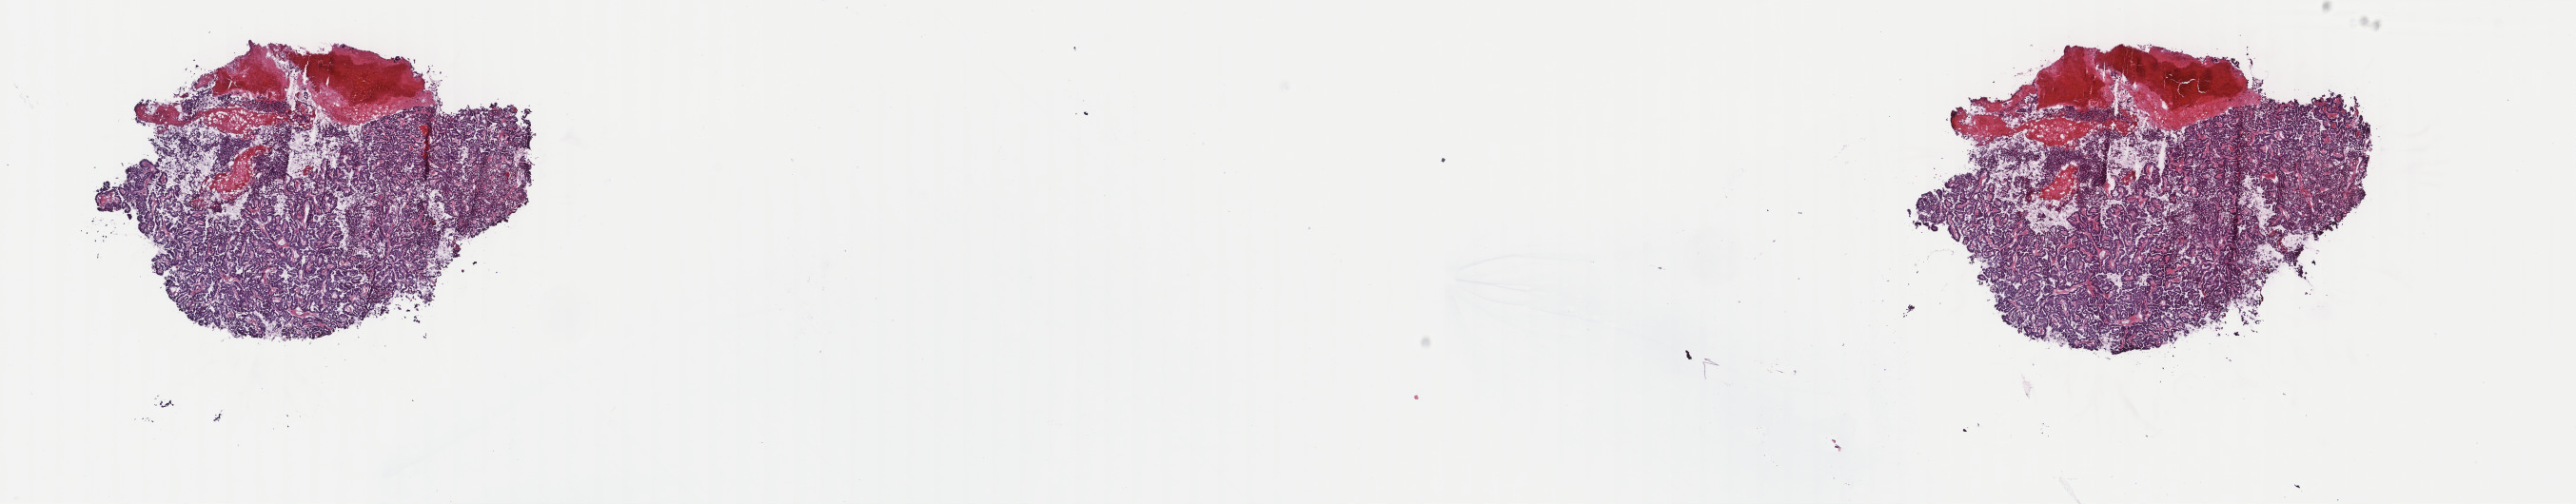
Whole-slide histology image, H&E — whole scanned area (about 21.5 x 4.2 mm, acquisition: 40x scan) shown as a low-resolution overview; frozen section; sample: primary tumour, thyroid. Male patient; age at initial diagnosis 71 years. Pathologist review of this section (percent, as recorded): tumour cells 75%, tumour nuclei 100%, normal cells 0%, stromal cells 25%, necrosis 0%. Inflammatory infiltration, as recorded: lymphocyte infiltration 2%, monocyte infiltration 2%, neutrophil infiltration 0%.
Lymph nodes positive (case pathology): 9 of 41 examined. AJCC pathologic stage: IVA (7th edition). Histologic diagnosis: Papillary adenocarcinoma, NOS (thyroid gland).